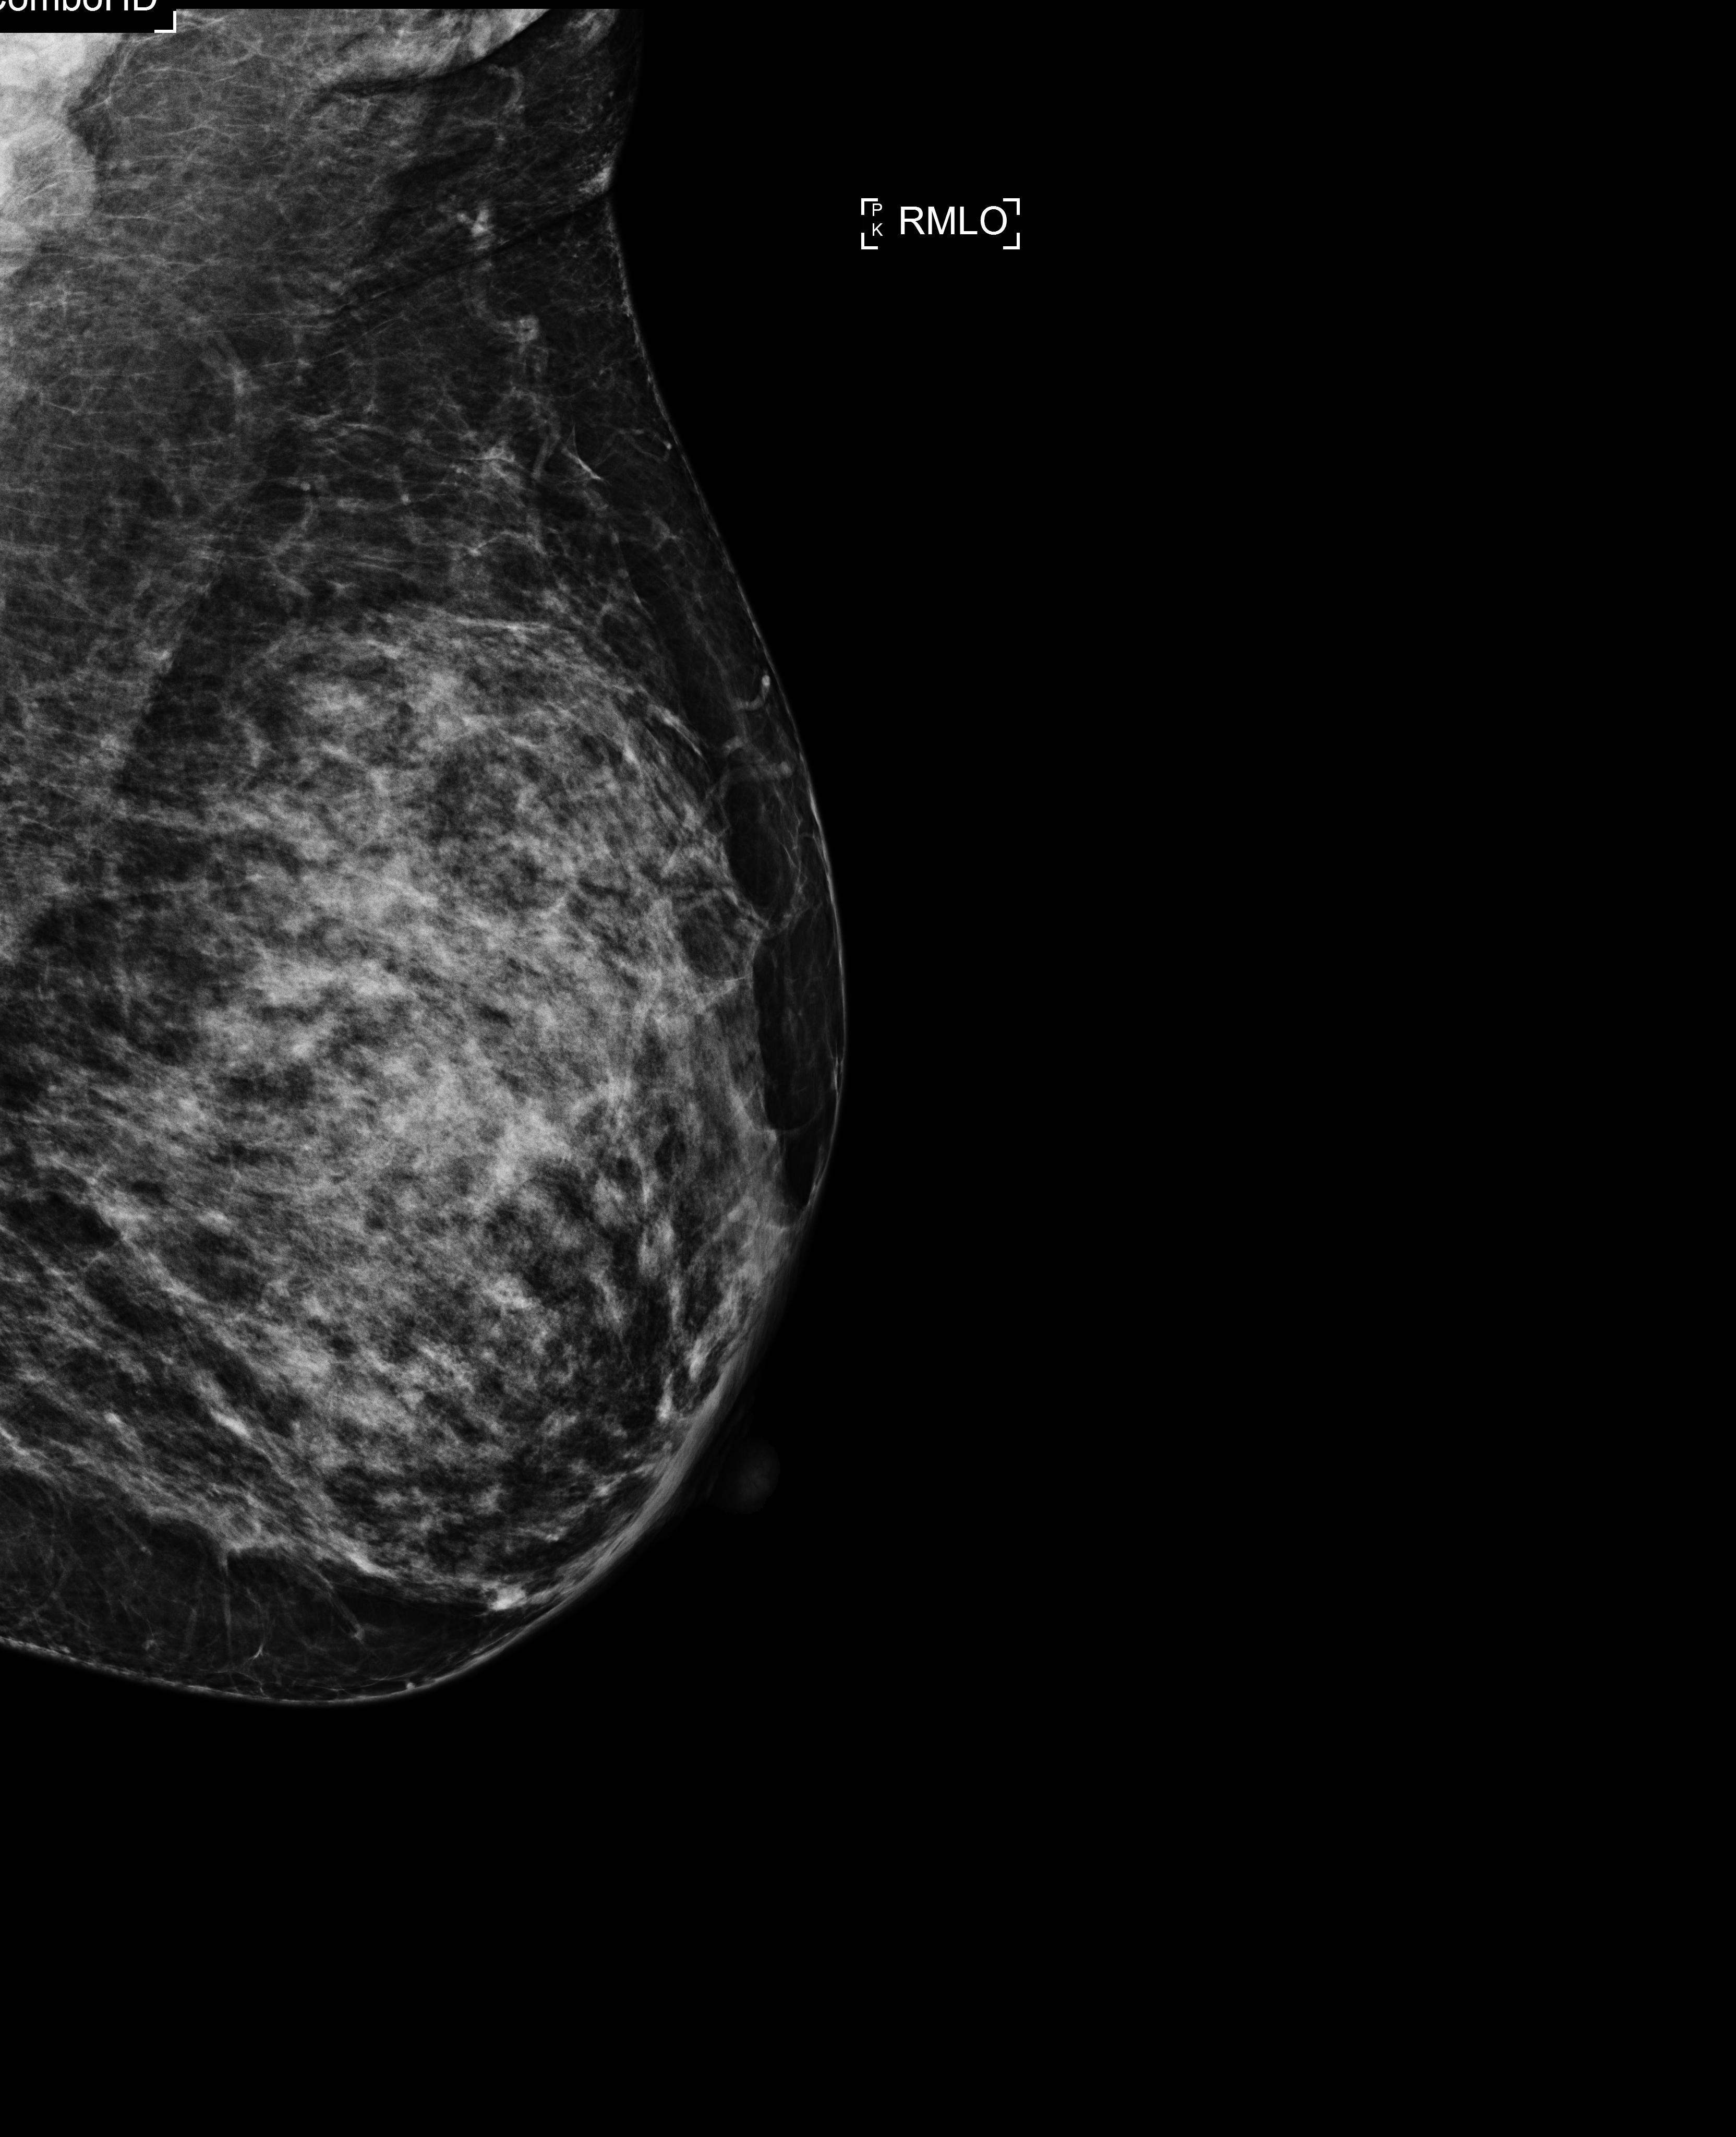
Screening examination; compressed breast thickness 75 mm; system: Selenia Dimensions. Patient: female, 43 years.
Image type: full-field digital mammogram. Breast: right. Projection: mediolateral oblique (MLO) view.